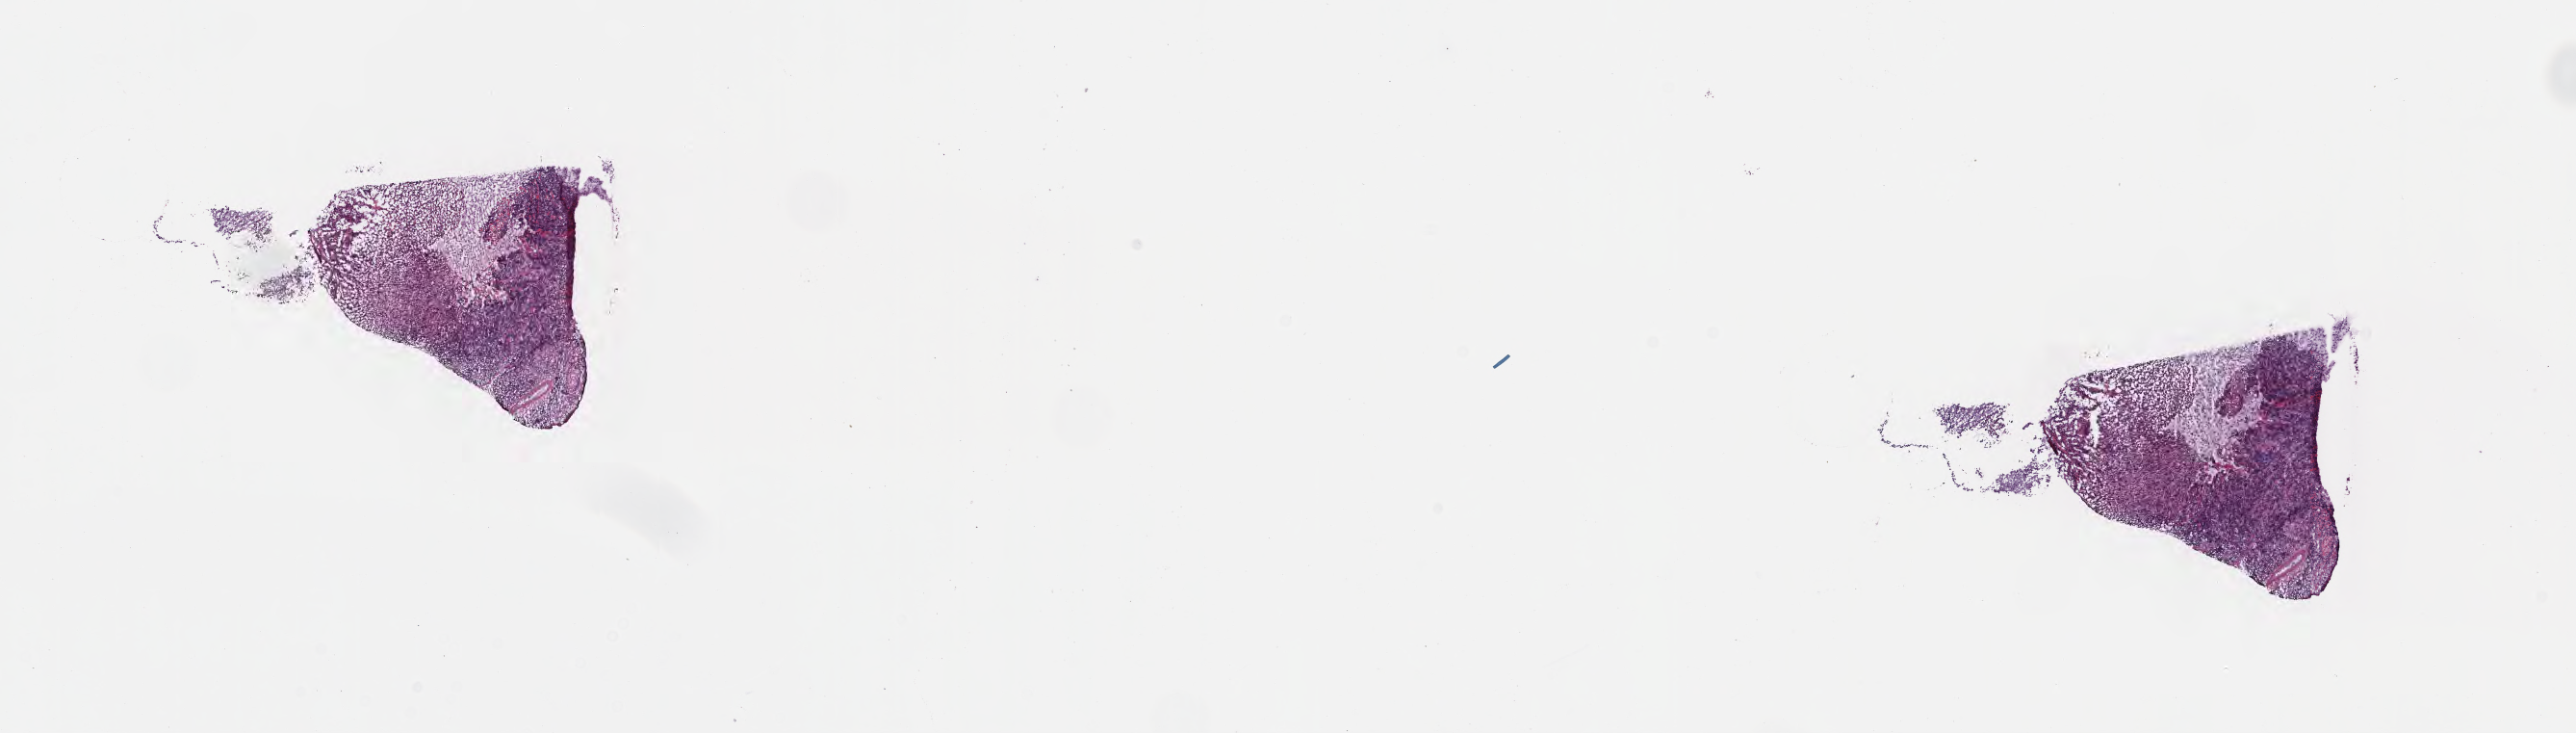
Hematoxylin and eosin (H&E) whole-slide image, shown as a low-resolution overview of the whole scanned area (about 21.6 x 6.2 mm). Frozen section. Specimen: primary tumor. Anatomic site: lip. Male patient; age at initial diagnosis 7 years. Pathologist review of this section (percent, as recorded): tumor cells 75%, tumor nuclei 75%, stromal cells 10%, necrosis 5%, normal cells 10%. Infiltration values recorded for this section: lymphocyte infiltration 60%, monocyte infiltration 20%, neutrophil infiltration 5%.
Diagnosis: Diffuse large B-cell lymphoma, NOS. Ann Arbor stage (patient): Stage II.